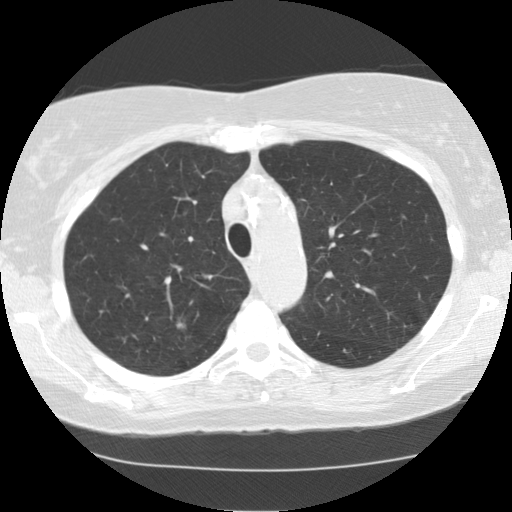
Axial slice from a low-dose chest CT screening exam. Baseline screening round. Lung window (W 1500 / L -600 HU). Standard (soft-tissue) reconstruction kernel (STANDARD). Slice 30 of 117 in the series. 512 × 512 image matrix. Female, age 72 years at enrolment.
Expert reader's lesion annotation, bounding box (x1, y1, x2, y2) in pixels: (160, 302, 198, 344). The screening reader recorded 5 non-calcified nodules or masses ≥4 mm on this exam; which of them this box marks is not recorded. Lung cancer was diagnosed 812 days after this screen (after the third annual screen): bronchiolo-alveolar adenocarcinoma, NOS, right upper lobe, well differentiated (G1), stage IA (AJCC 6th edition), 8 mm at pathology.